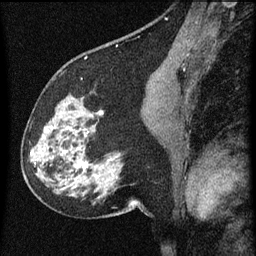
Breast MRI (dynamic contrast-enhanced), one sagittal slice; dynamic contrast-enhanced series, image 2 of 3 at this slice position (ordered by acquisition); 1.5 T; TE 4.2 ms, TR 8 ms; 2 mm slice thickness; 256 × 256 image matrix, field of view 180 × 180 mm. Female patient, age 61 years.
Structures marked on this image (semi-automatic segmentation, software-assisted and operator-edited):
- analysis volume of interest (the breast-tissue region the enhancement analysis was run in; not a lesion): bounding box [x1, y1, x2, y2] px = [27, 82, 139, 209]
- tumour enhancement mask (voxels above the 70 % enhancement threshold inside the analysis volume of interest): [30, 112, 98, 165]